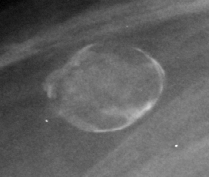
Region of interest cut from a scanned film mammogram (one marked finding), right breast, CC view, BI-RADS breast density category 1 (scale 1–4).
- Finding: calcifications, morphology eggshell; BI-RADS assessment category 2; benign without callback (not worked up further).